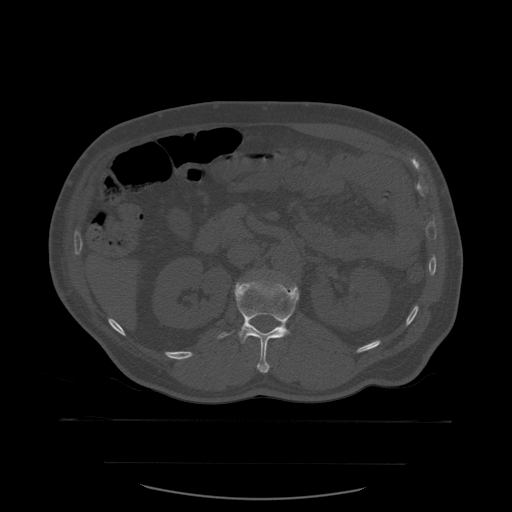
CT including the spine, one axial slice. Slice 244 of 590 in the series (ordered by position). Bone window (W 1800 / L 400 HU). 512 × 512 image matrix, field of view 479 × 479 mm. Patient age 71 years. From the clinical record (not read from this slice): primary cancer: lung; vertebrae with lytic lesions (as recorded): T1, T2, L5, S1.
Annotated regions visible in this slice (semi-automatically segmented with operator editing):
- L1 vertebra: bounding box [x1, y1, x2, y2] px = [217, 277, 300, 373]